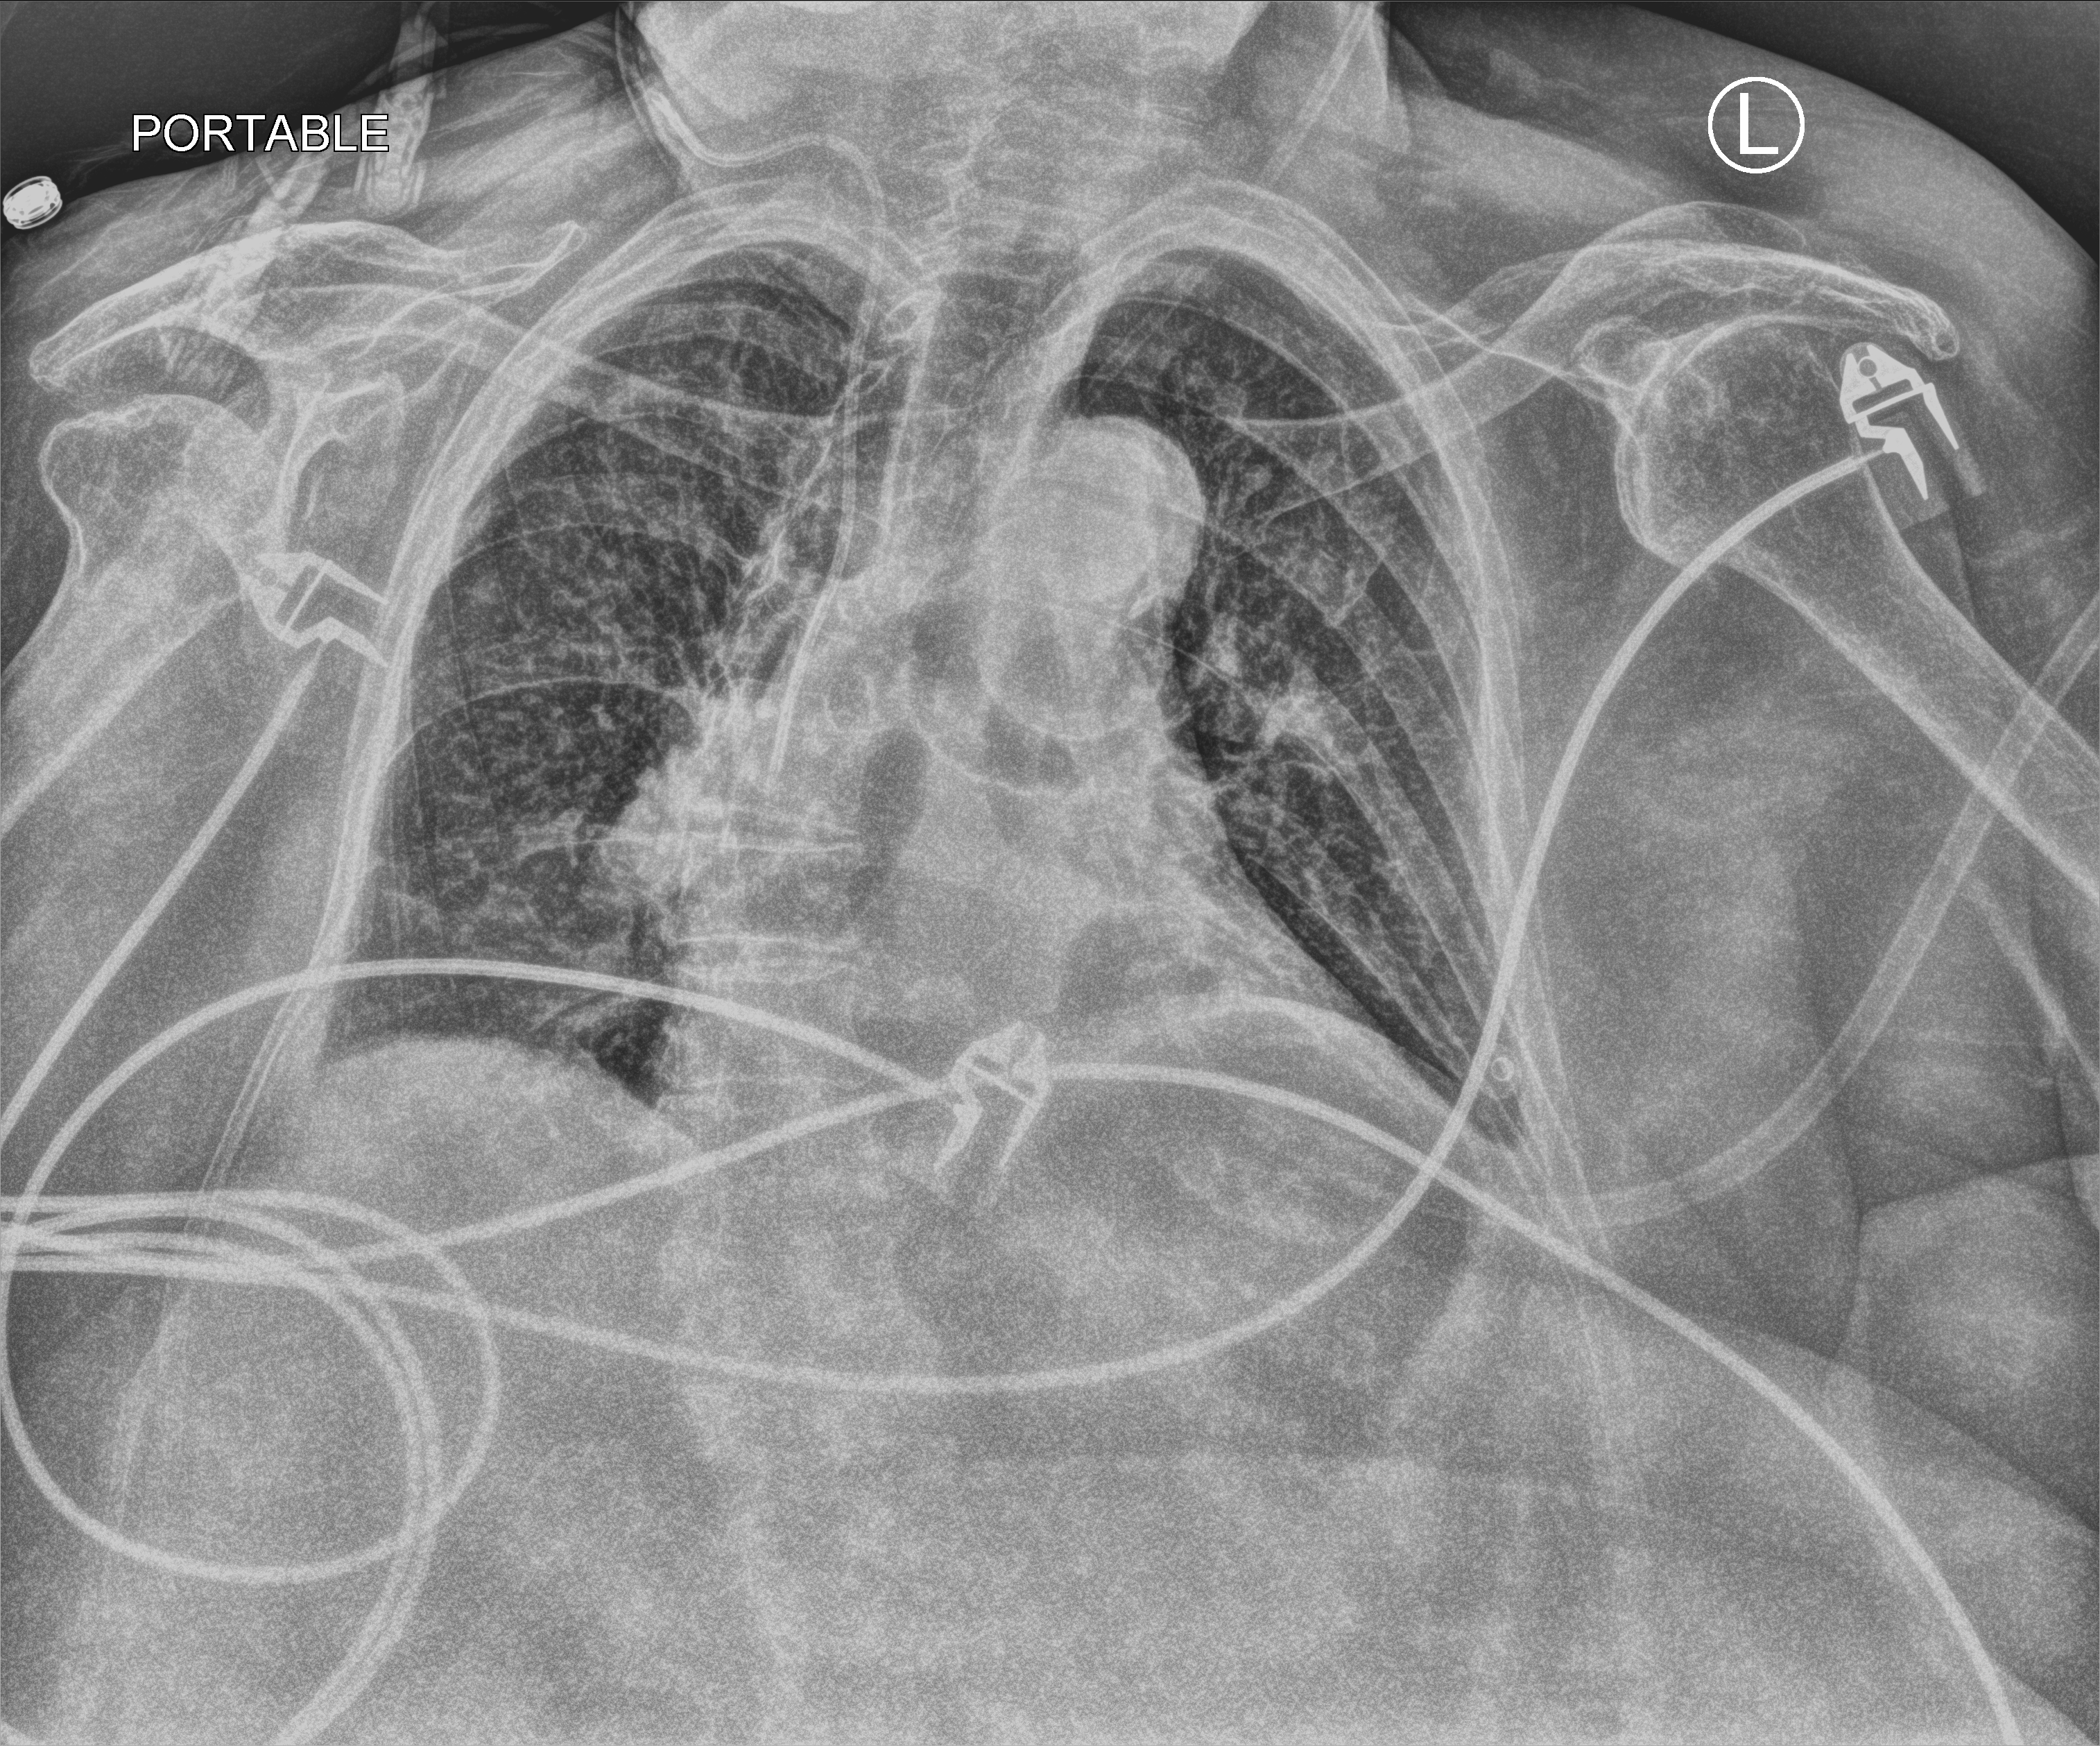
Chest X-ray (portable), anteroposterior (AP) projection. Patient hospitalised with COVID-19; female, aged 75–90 years.
Admission-level facts for this patient (not findings on this image; timing relative to this image not recorded): length of hospital stay: 12 days.